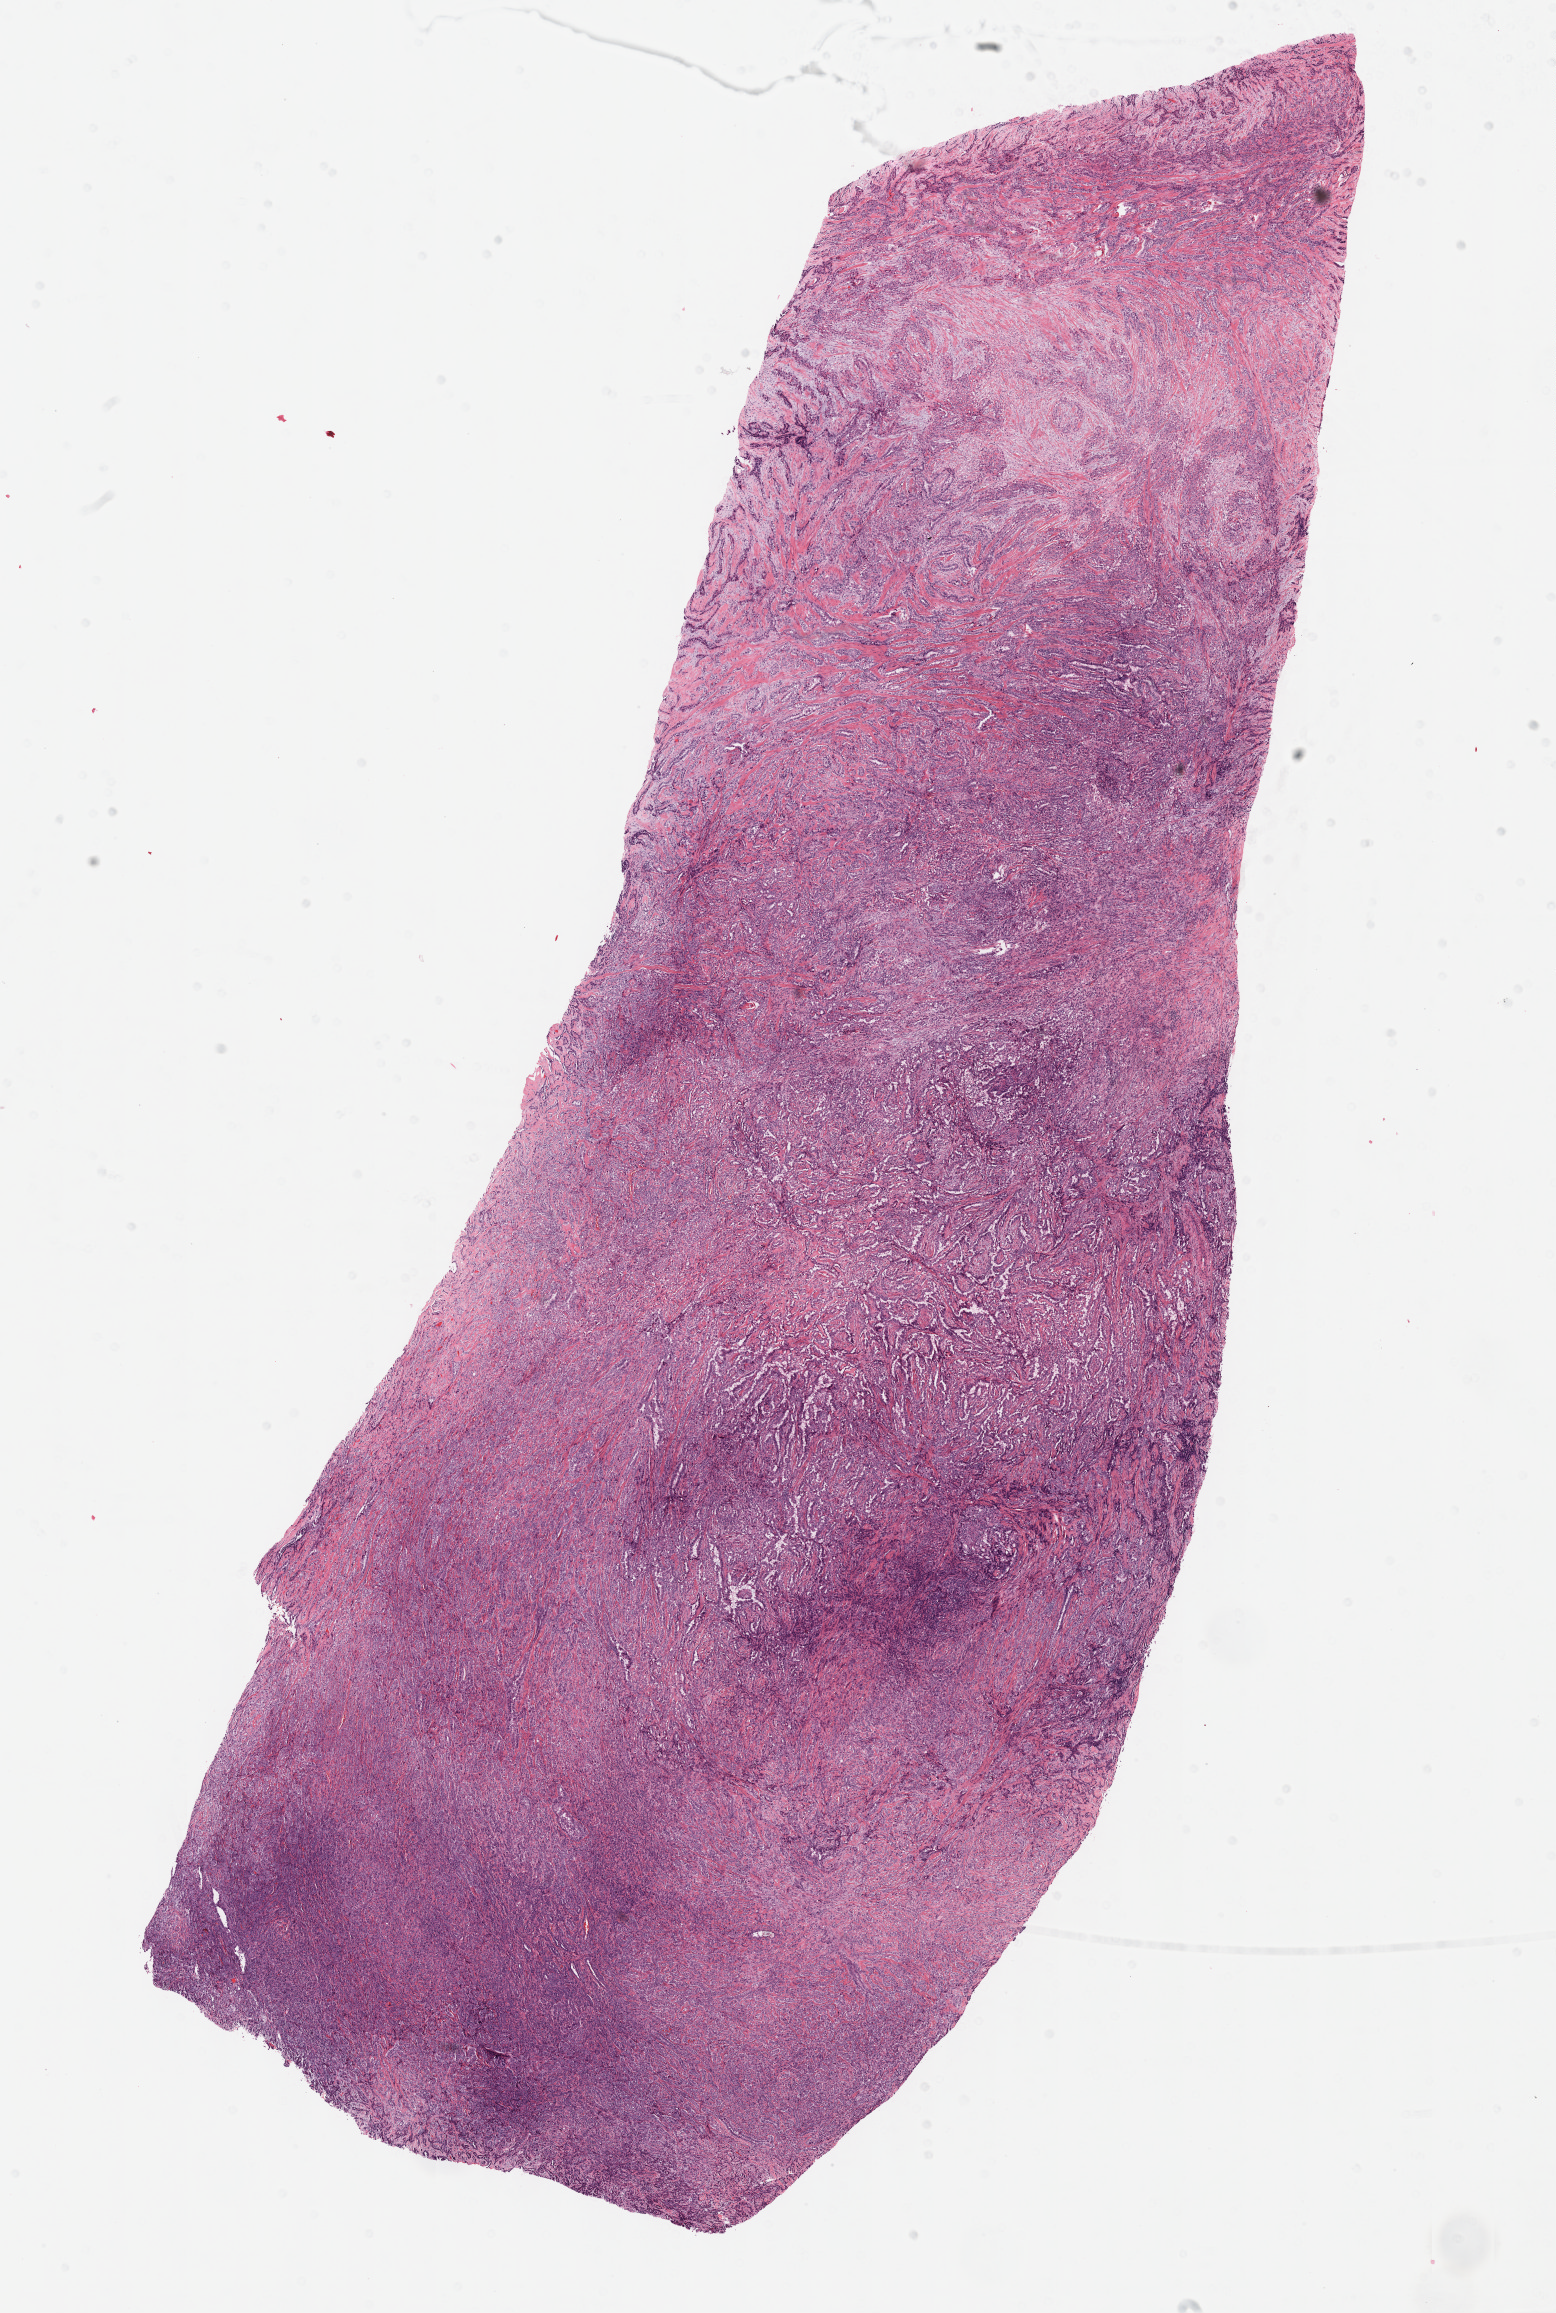
H&E-stained whole-slide image — a low-resolution overview of the entire scanned area, about 12.6 x 18.7 mm. Formalin-fixed paraffin-embedded (FFPE) diagnostic section. Primary tumour sample from the mesothelium. Male patient; age at initial diagnosis 42 years.
Histologic diagnosis: Epithelioid mesothelioma, malignant. AJCC pathologic stage: III (6th edition).